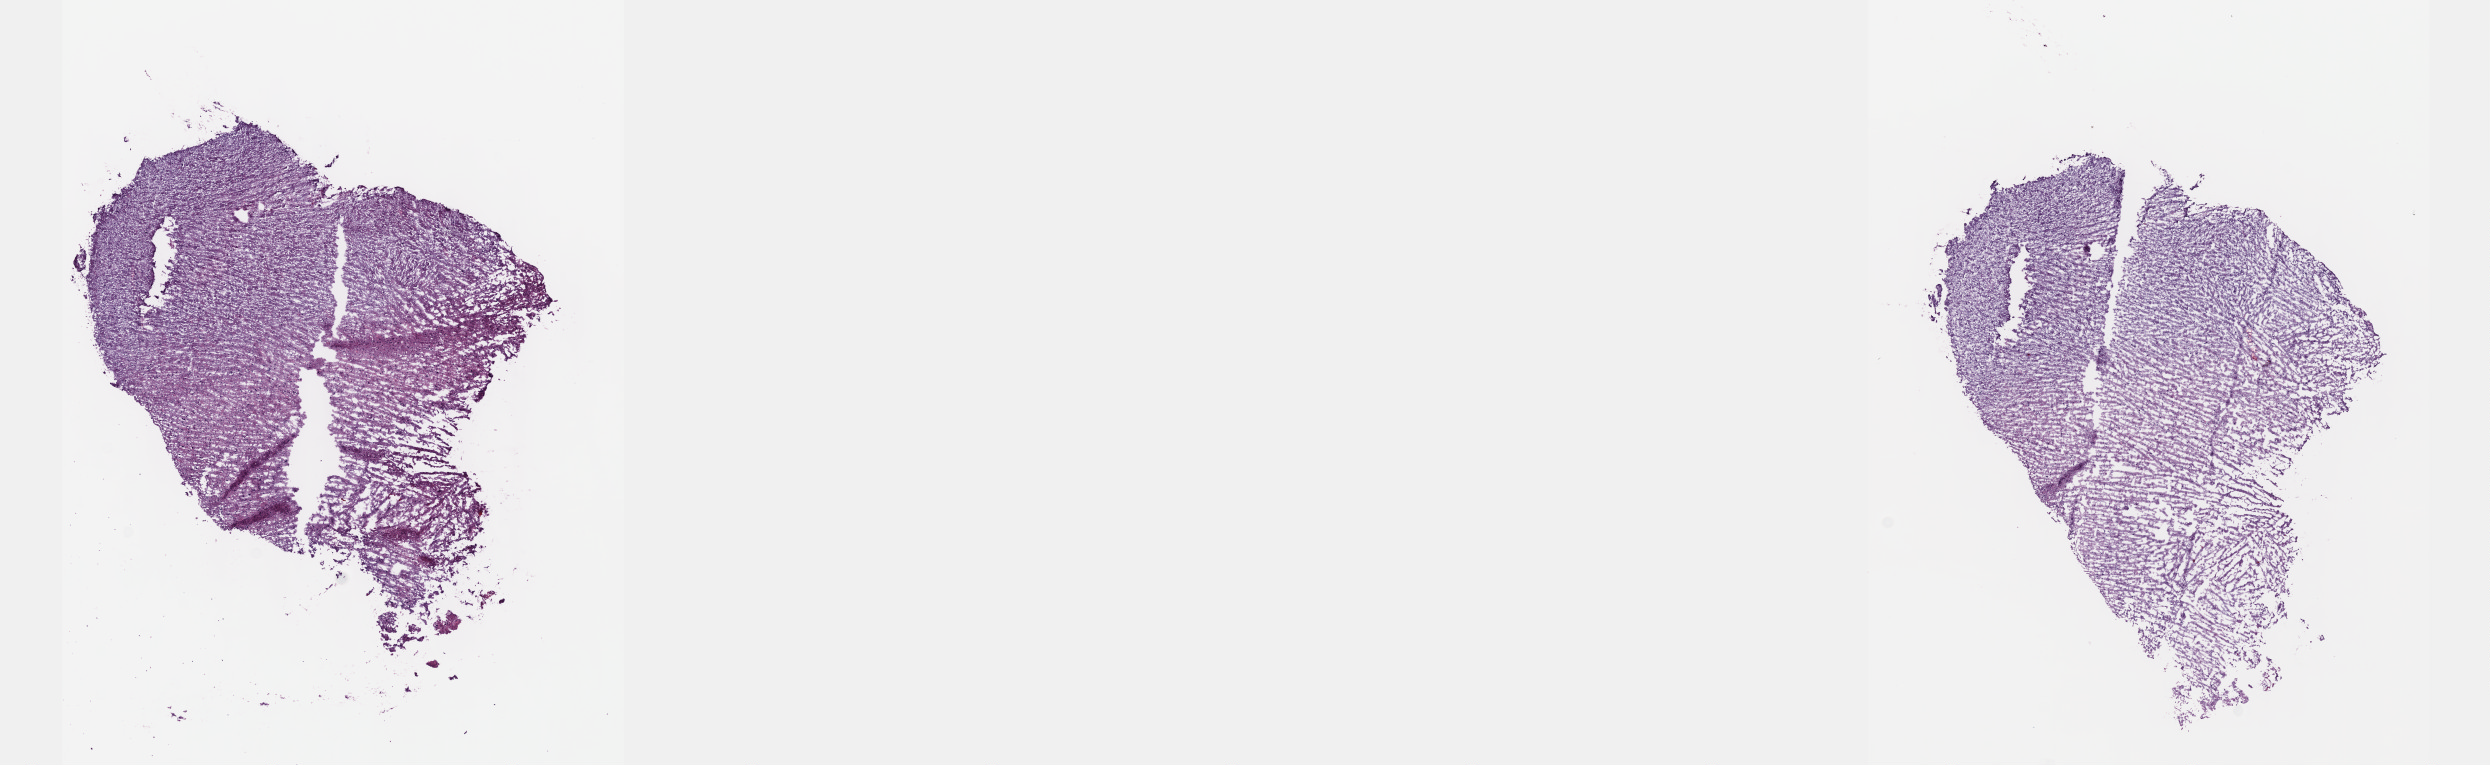
H&E whole-slide image — a low-resolution overview of the entire scanned area, about 20.1 x 6.2 mm (from a 40x scan), frozen section from the top of the tissue portion, recurrent tumour sample from the brain. Patient: female, age at initial diagnosis 41 years. Composition of this section per pathologist review: tumour cells 25%, tumour nuclei 70%, normal cells 10%, stromal cells 65%, necrosis 0%. Inflammatory infiltration, as recorded: lymphocyte infiltration 0%, monocyte infiltration 0%, neutrophil infiltration 0%.
This section: recurrent tumour. Patient diagnosis: Astrocytoma, NOS (cerebrum).